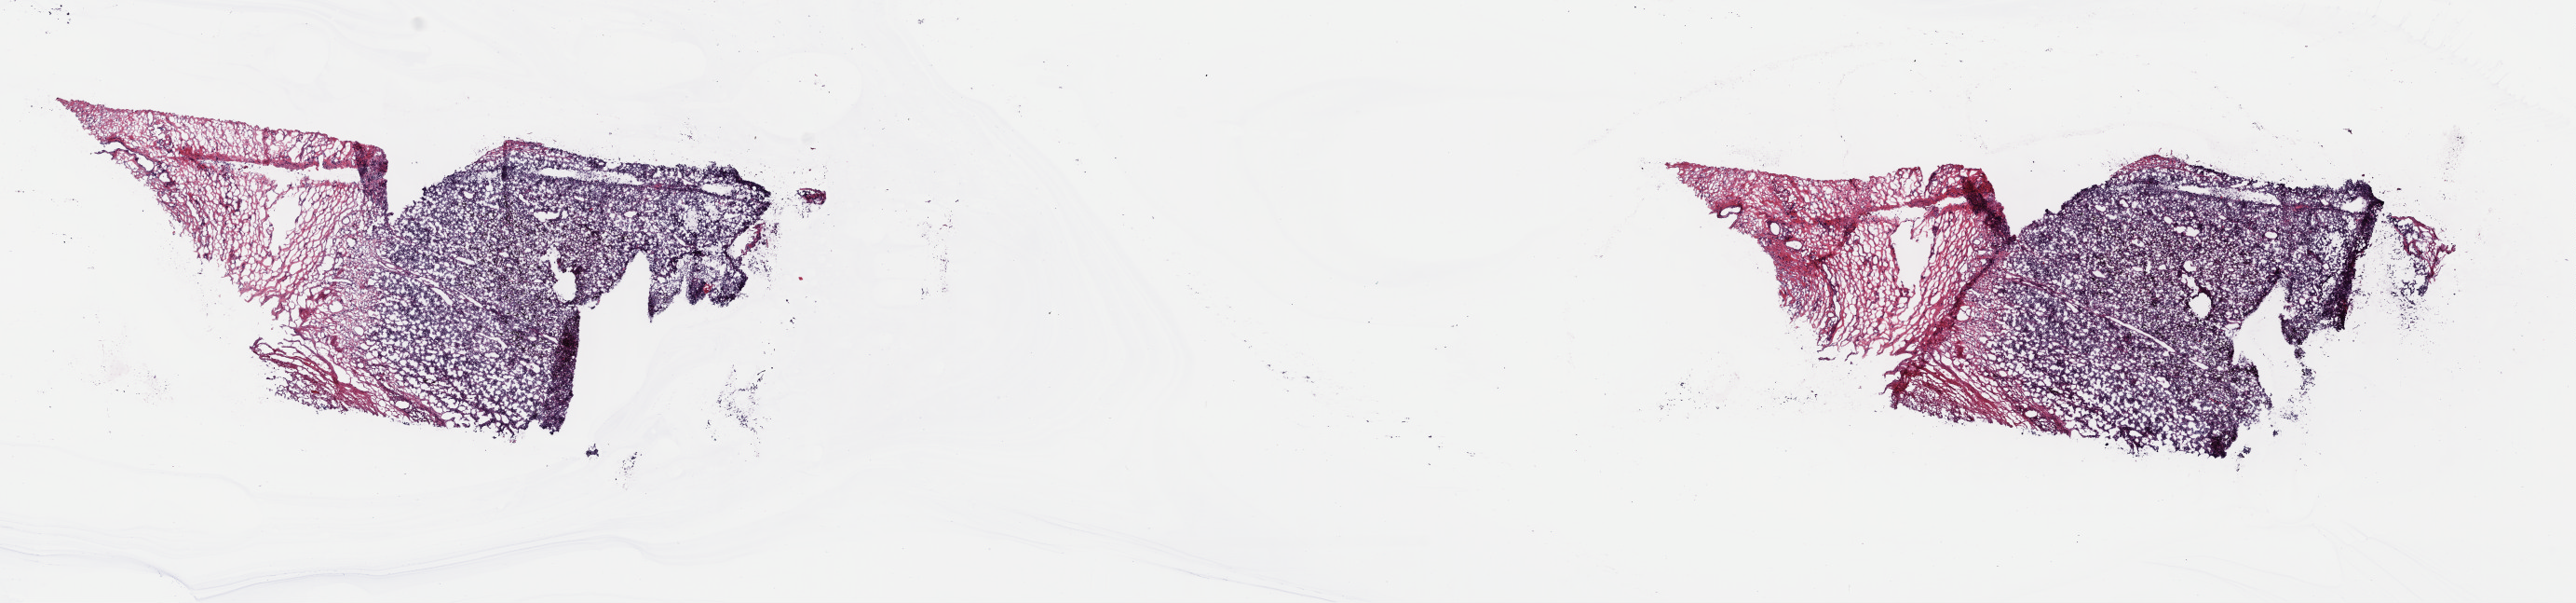
Digitized H&E-stained tissue section (whole slide), a low-resolution overview of the entire scanned area, about 21.7 x 5.1 mm (from a 40x scan). Frozen section. Sample: primary tumour, esophagus. Patient: male, age at initial diagnosis 56 years. Histologic grade: G2 (moderately differentiated). Slide review estimates, as recorded: tumour cells 65%, tumour nuclei 88%, normal cells 25%, stromal cells 10%, necrosis 0%. Inflammatory infiltration, as recorded: lymphocyte infiltration 0%, monocyte infiltration 0%, neutrophil infiltration 0%.
- AJCC pathologic stage: IIA
- diagnosis: Squamous cell carcinoma, keratinizing, NOS (thoracic esophagus)
- lymph nodes positive (case pathology): 0 of 17 examined
- TNM: T3 N0 M0